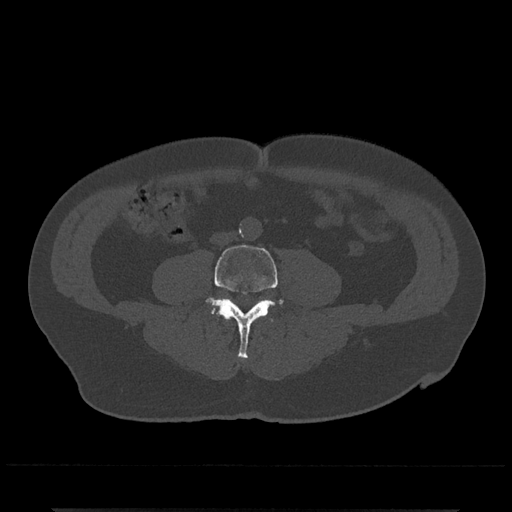
CT including the spine, one axial slice. Position 147 of 797 along the scan axis. Reconstruction kernel Br40s/3. 120 kVp. Bone window (W 1800 / L 400 HU). 0.5 mm slice thickness. 512 × 512 image matrix, field of view 393 × 393 mm. Male patient, age 67 years. From the clinical record (not read from this slice): primary cancer: prostate.
Outlined on this slice (semi-automatic segmentation, software-assisted and operator-edited):
- L4 vertebra: bounding box <206,244,284,359> (left, top, right, bottom; pixels)